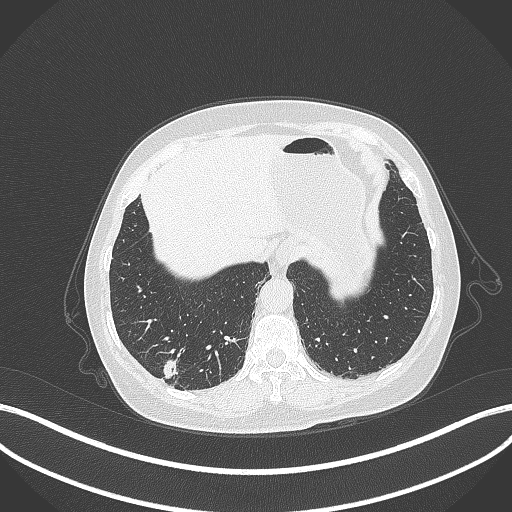
Chest CT, one axial slice. Slice 51 of 333 in the series (ordered by position). Lung window (W 1500 / L -600 HU). 512 × 512 image matrix, field of view 400 × 400 mm. Patient: female, 69 years. Case-level facts recorded for this patient, not image findings: clinical TNM (as recorded): T1b N0 M0; histopathological grade: G2-3.
Structures marked on this image (bounding box drawn by a radiologist):
- lung tumour (recorded histology: adenocarcinoma): box from (x=158, y=357) to (x=178, y=382) px